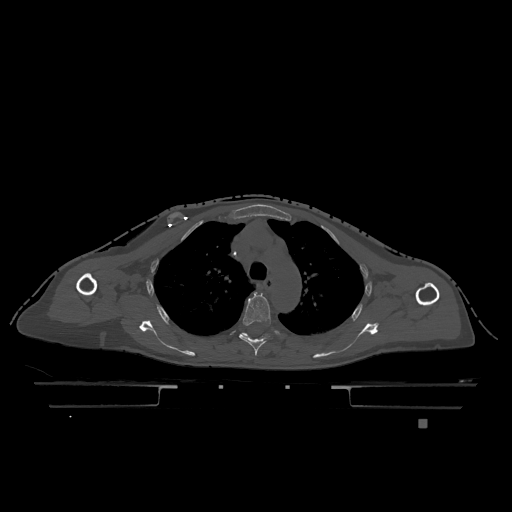
CT including the spine, one axial slice; slice 875 of 1317 in the series (ordered by position); bone window (W 1800 / L 400 HU); 512 × 512 image matrix, field of view 500 × 500 mm. Female patient, age 74 years. Case-level facts recorded for this patient, not image findings: primary cancer: lung; vertebrae with lytic lesions (as recorded): T1, T4, T5, T6, L4, L5.
Outlined on this slice (semi-automatically segmented with operator editing):
- T4 vertebra: bounding box <239,293,273,356> (left, top, right, bottom; pixels)
- T5 vertebra: <242,333,248,337>